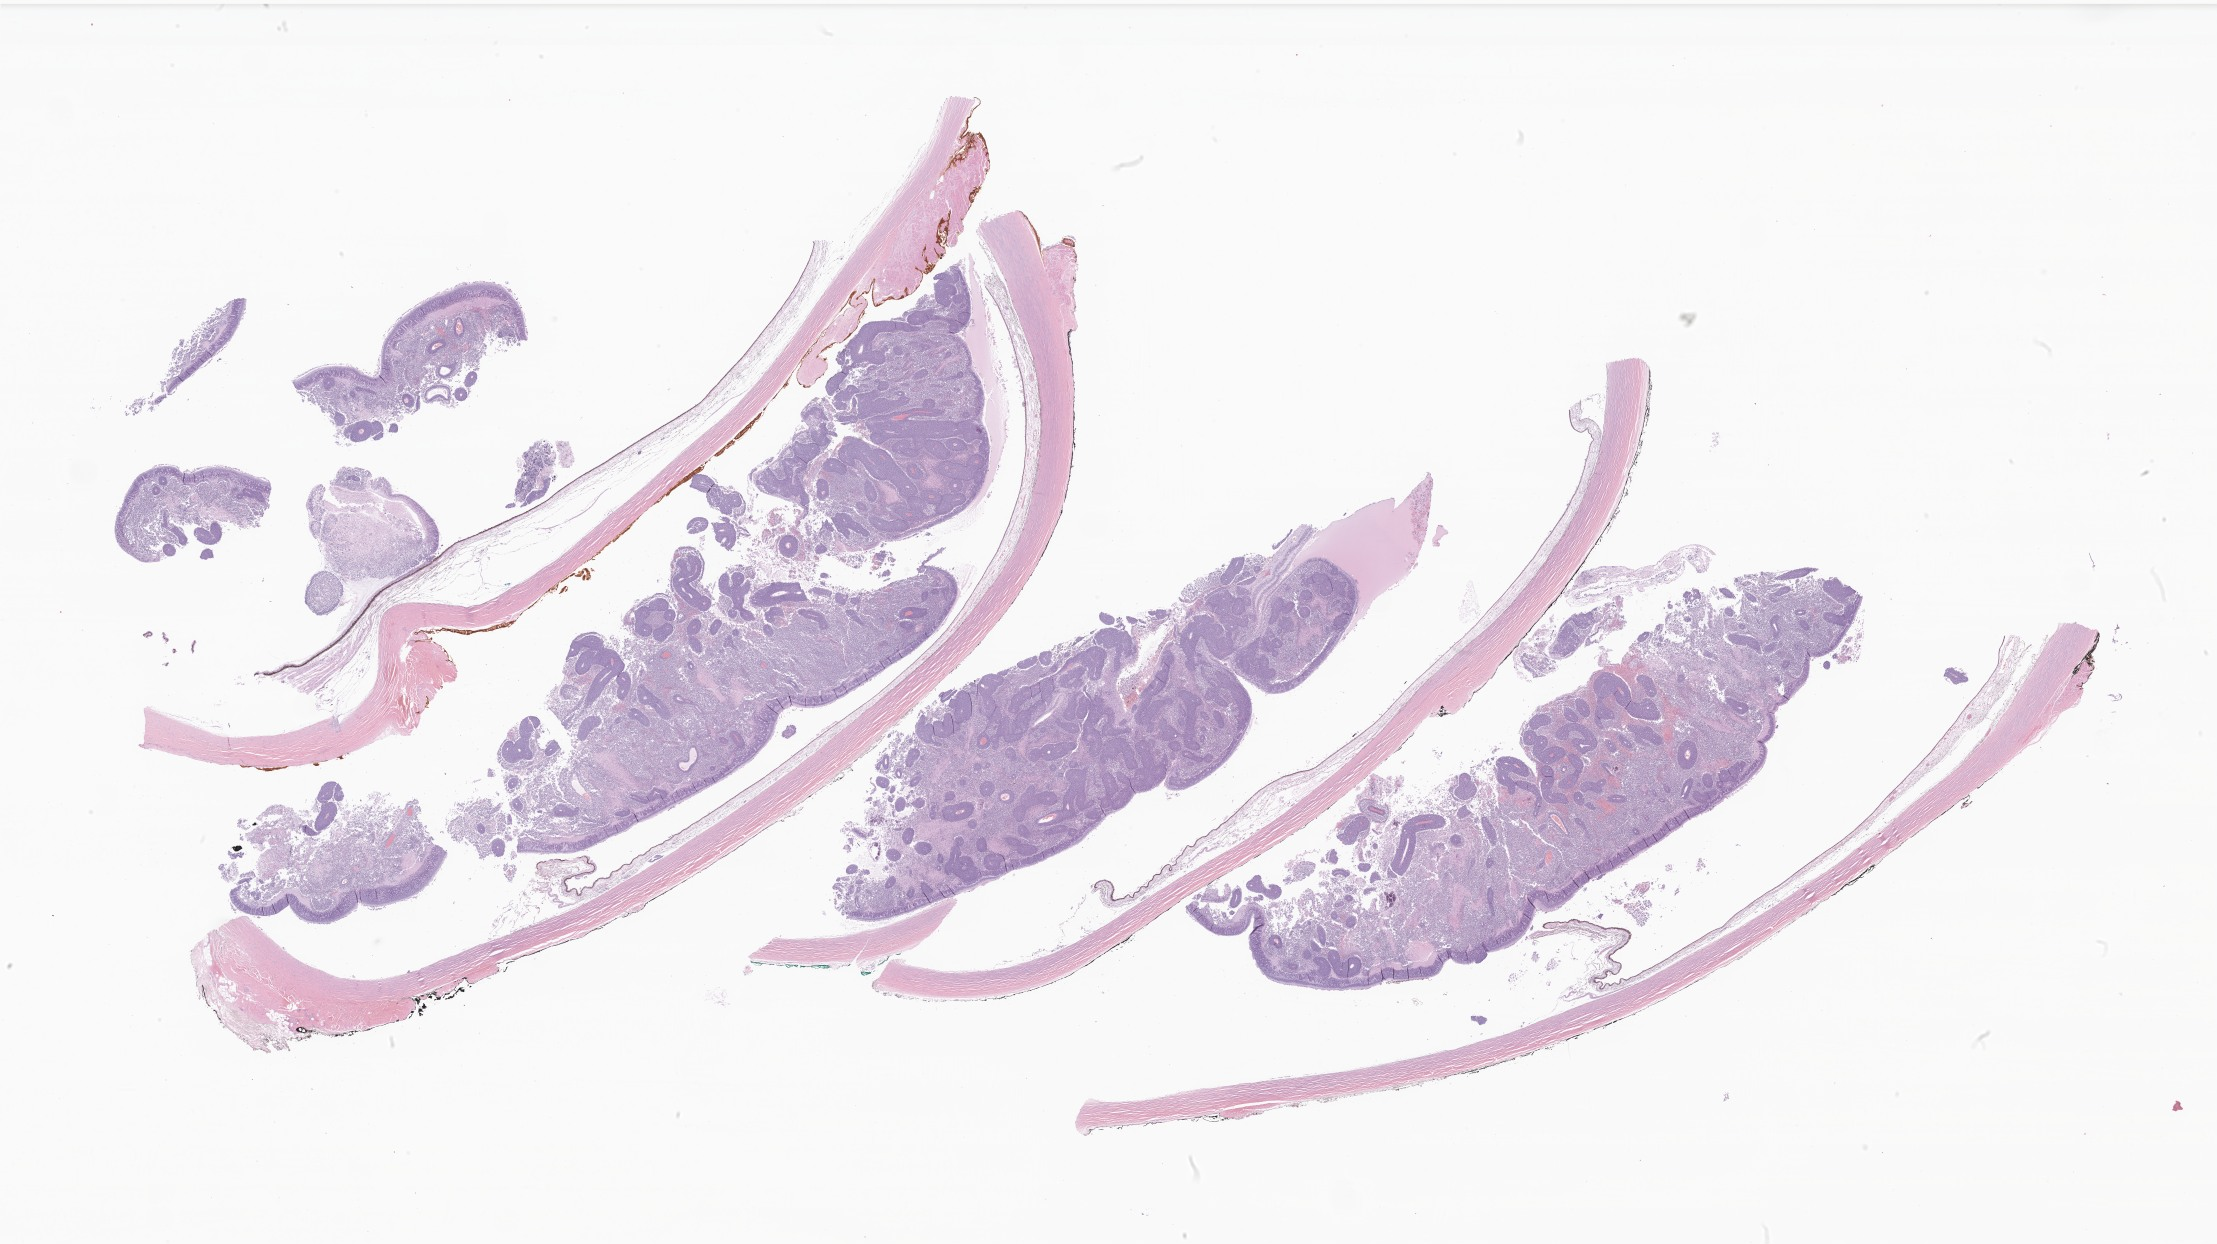
Whole-slide image, haematoxylin and eosin stain of tumor tissue from the eye — low-resolution overview of the scanned area, about 37.4 x 21.0 mm; formalin-fixed, paraffin-embedded (FFPE) tissue. Male patient, age 47 months (3 years 11 months).
Diagnosis (ICD-O-3 morphology term): Retinoblastoma, NOS.